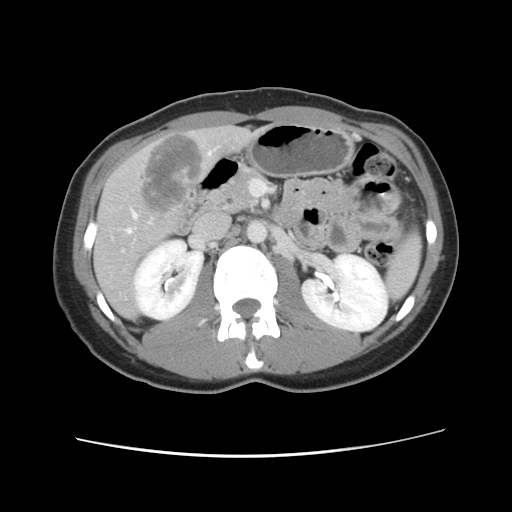
Contrast-enhanced abdominal CT, one axial slice; position 45 of 134 along the scan axis; intravenous contrast given; soft-tissue window (W 400 / L 40 HU); 2.5 mm slice thickness; 512 × 512 image matrix, field of view 339 × 339 mm. Female patient, age 33 years. Case-level facts recorded for this patient, not image findings: diagnosis: colorectal cancer liver metastases, imaged before liver resection.
Annotated regions visible in this slice (expert manual segmentation):
- hepatic veins: box from (x=126, y=152) to (x=212, y=233) px
- liver: (x=94, y=127)–(x=257, y=317)
- planned liver remnant (the part of the liver to remain after resection): (x=93, y=131)–(x=257, y=317)
- liver metastasis: (x=139, y=134)–(x=205, y=216)